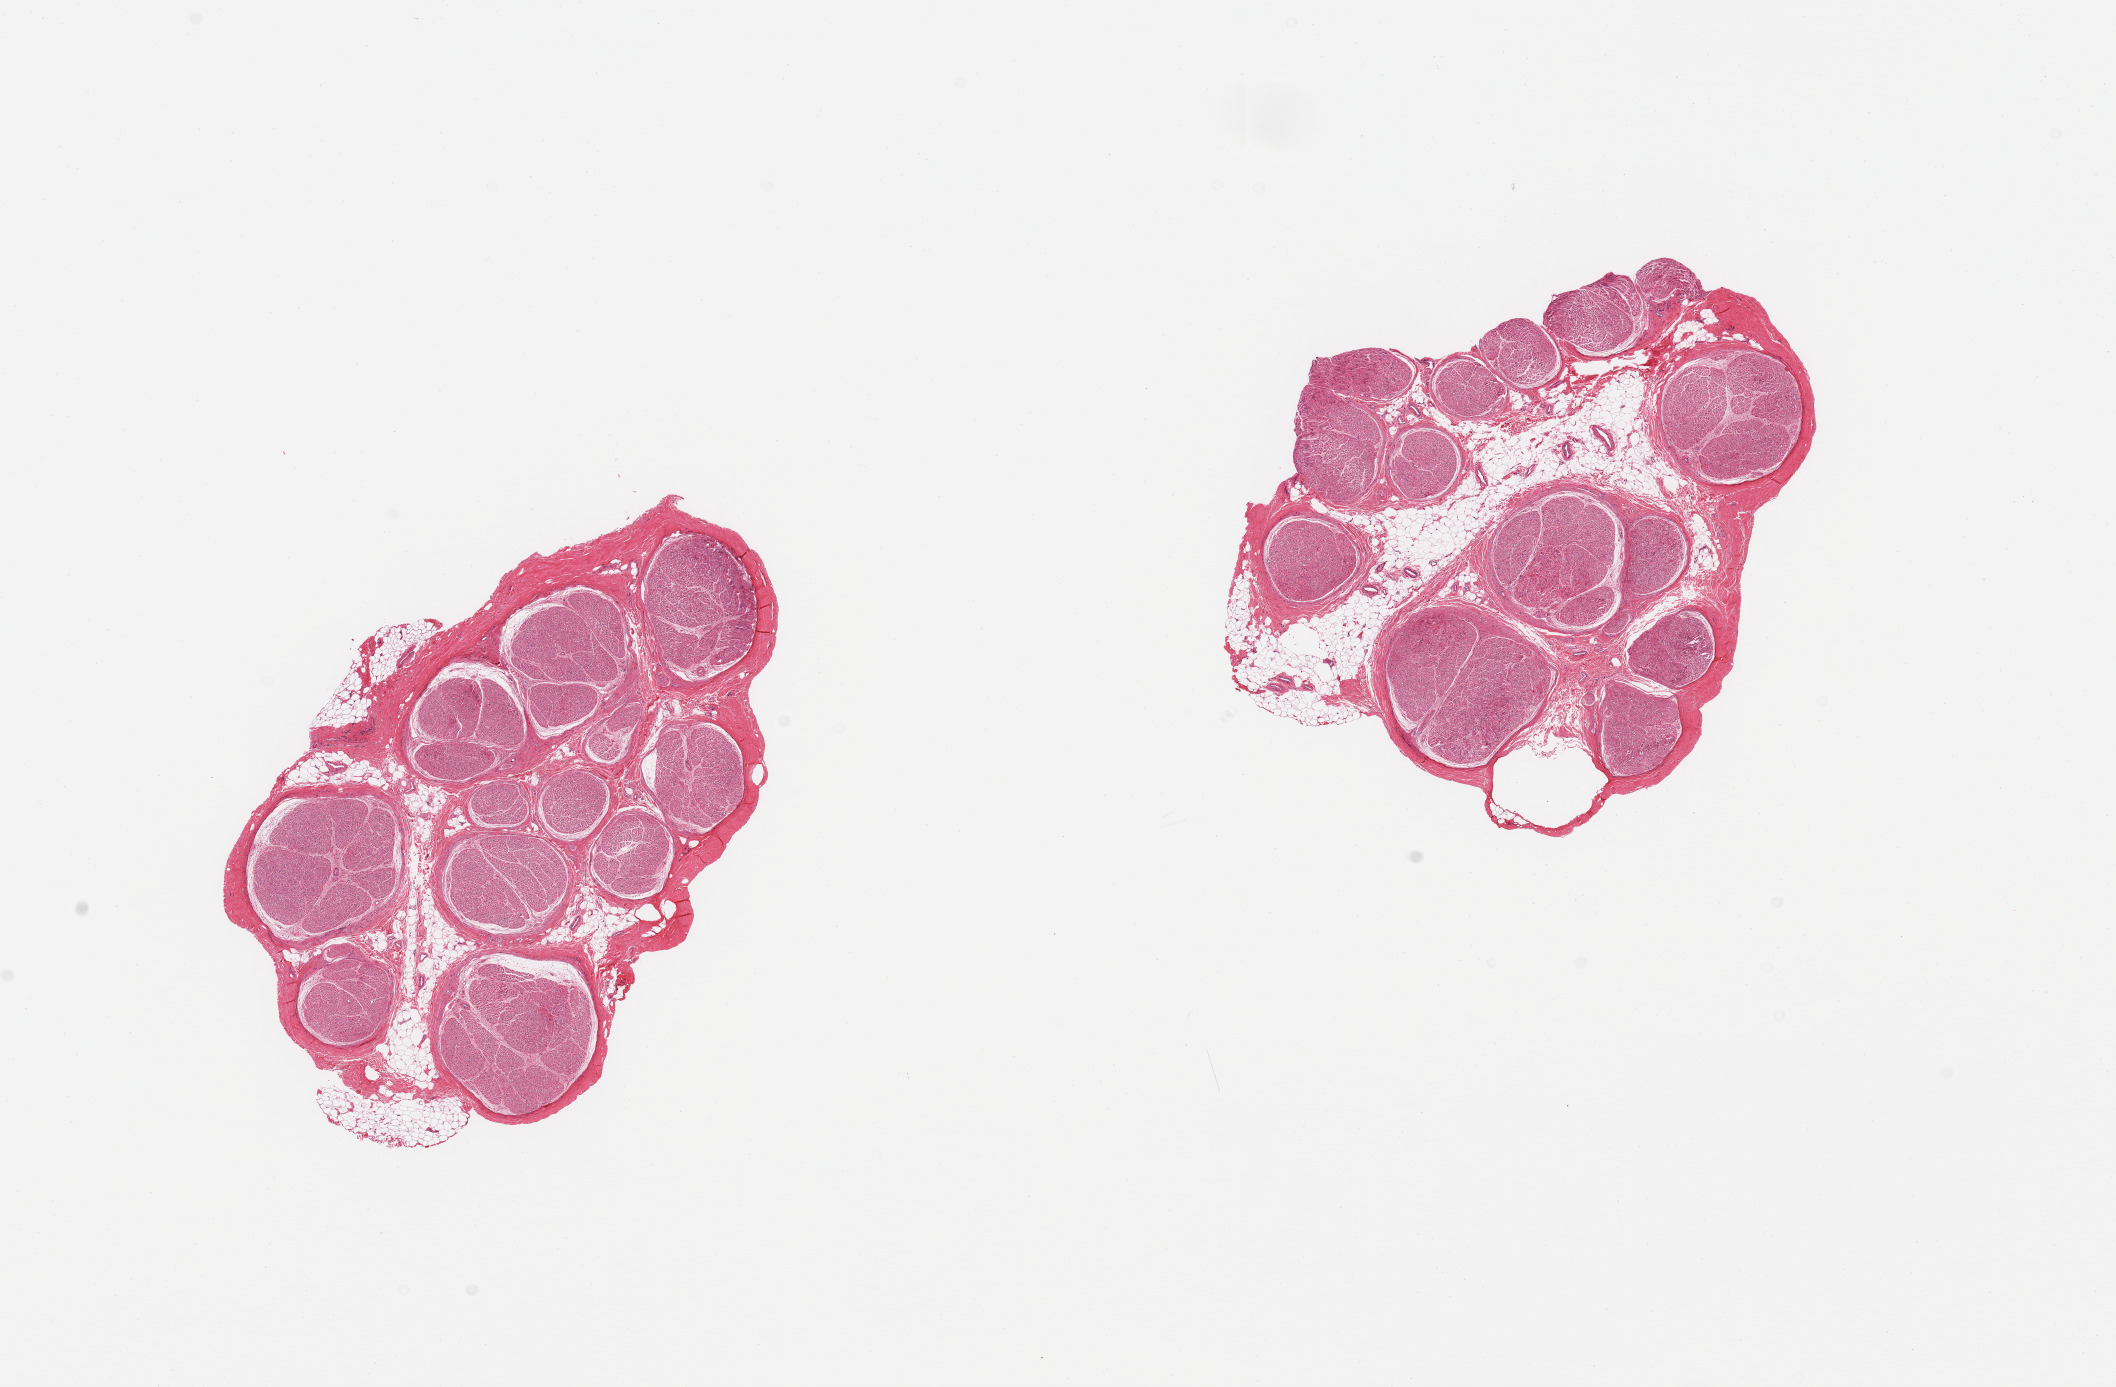
Haematoxylin and eosin whole-slide image, brightfield, a low-resolution overview of the entire scanned area, about 16.7 x 11.0 mm; PAXgene-fixed, paraffin-embedded tissue; section of tibial nerve (target tissue); donor tissue sample. Donor sex: male.
• review note (as recorded): 2 pieces, minute nubbins of adherent fat